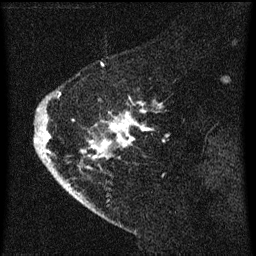
Breast MRI (dynamic contrast-enhanced), one sagittal slice. Slice 16 of 60 in the series (ordered by position). Dynamic contrast-enhanced series, image 2 of 3 at this slice position (ordered by acquisition). 1.5 T. TE 4.2 ms, TR 8 ms. 2 mm slice thickness. 256 × 256 image matrix, field of view 180 × 180 mm. Patient: female, 47 years.
Annotated regions visible in this slice (semi-automatically segmented with operator editing):
- analysis volume of interest (the breast-tissue region the enhancement analysis was run in; not a lesion): box from (x=38, y=76) to (x=161, y=193) px
- tumour enhancement mask (voxels above the 70 % enhancement threshold inside the analysis volume of interest): (x=39, y=92)–(x=161, y=189)